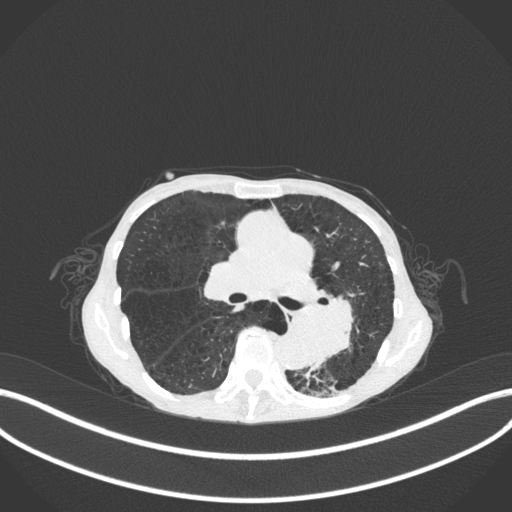
Chest CT, one axial slice; position 161 of 347 along the scan axis; reconstruction kernel B31f; 120 kVp; lung window (W 1500 / L -600 HU); 512 × 512 image matrix, field of view 400 × 400 mm. Patient: female, 70 years. From the clinical record (not read from this slice): clinical TNM (as recorded): T3 N0 M0; histopathological grade: G3.
Annotated regions visible in this slice (bounding box drawn by a radiologist):
- lung tumour (recorded histology: small cell carcinoma): box from (x=288, y=286) to (x=367, y=368) px